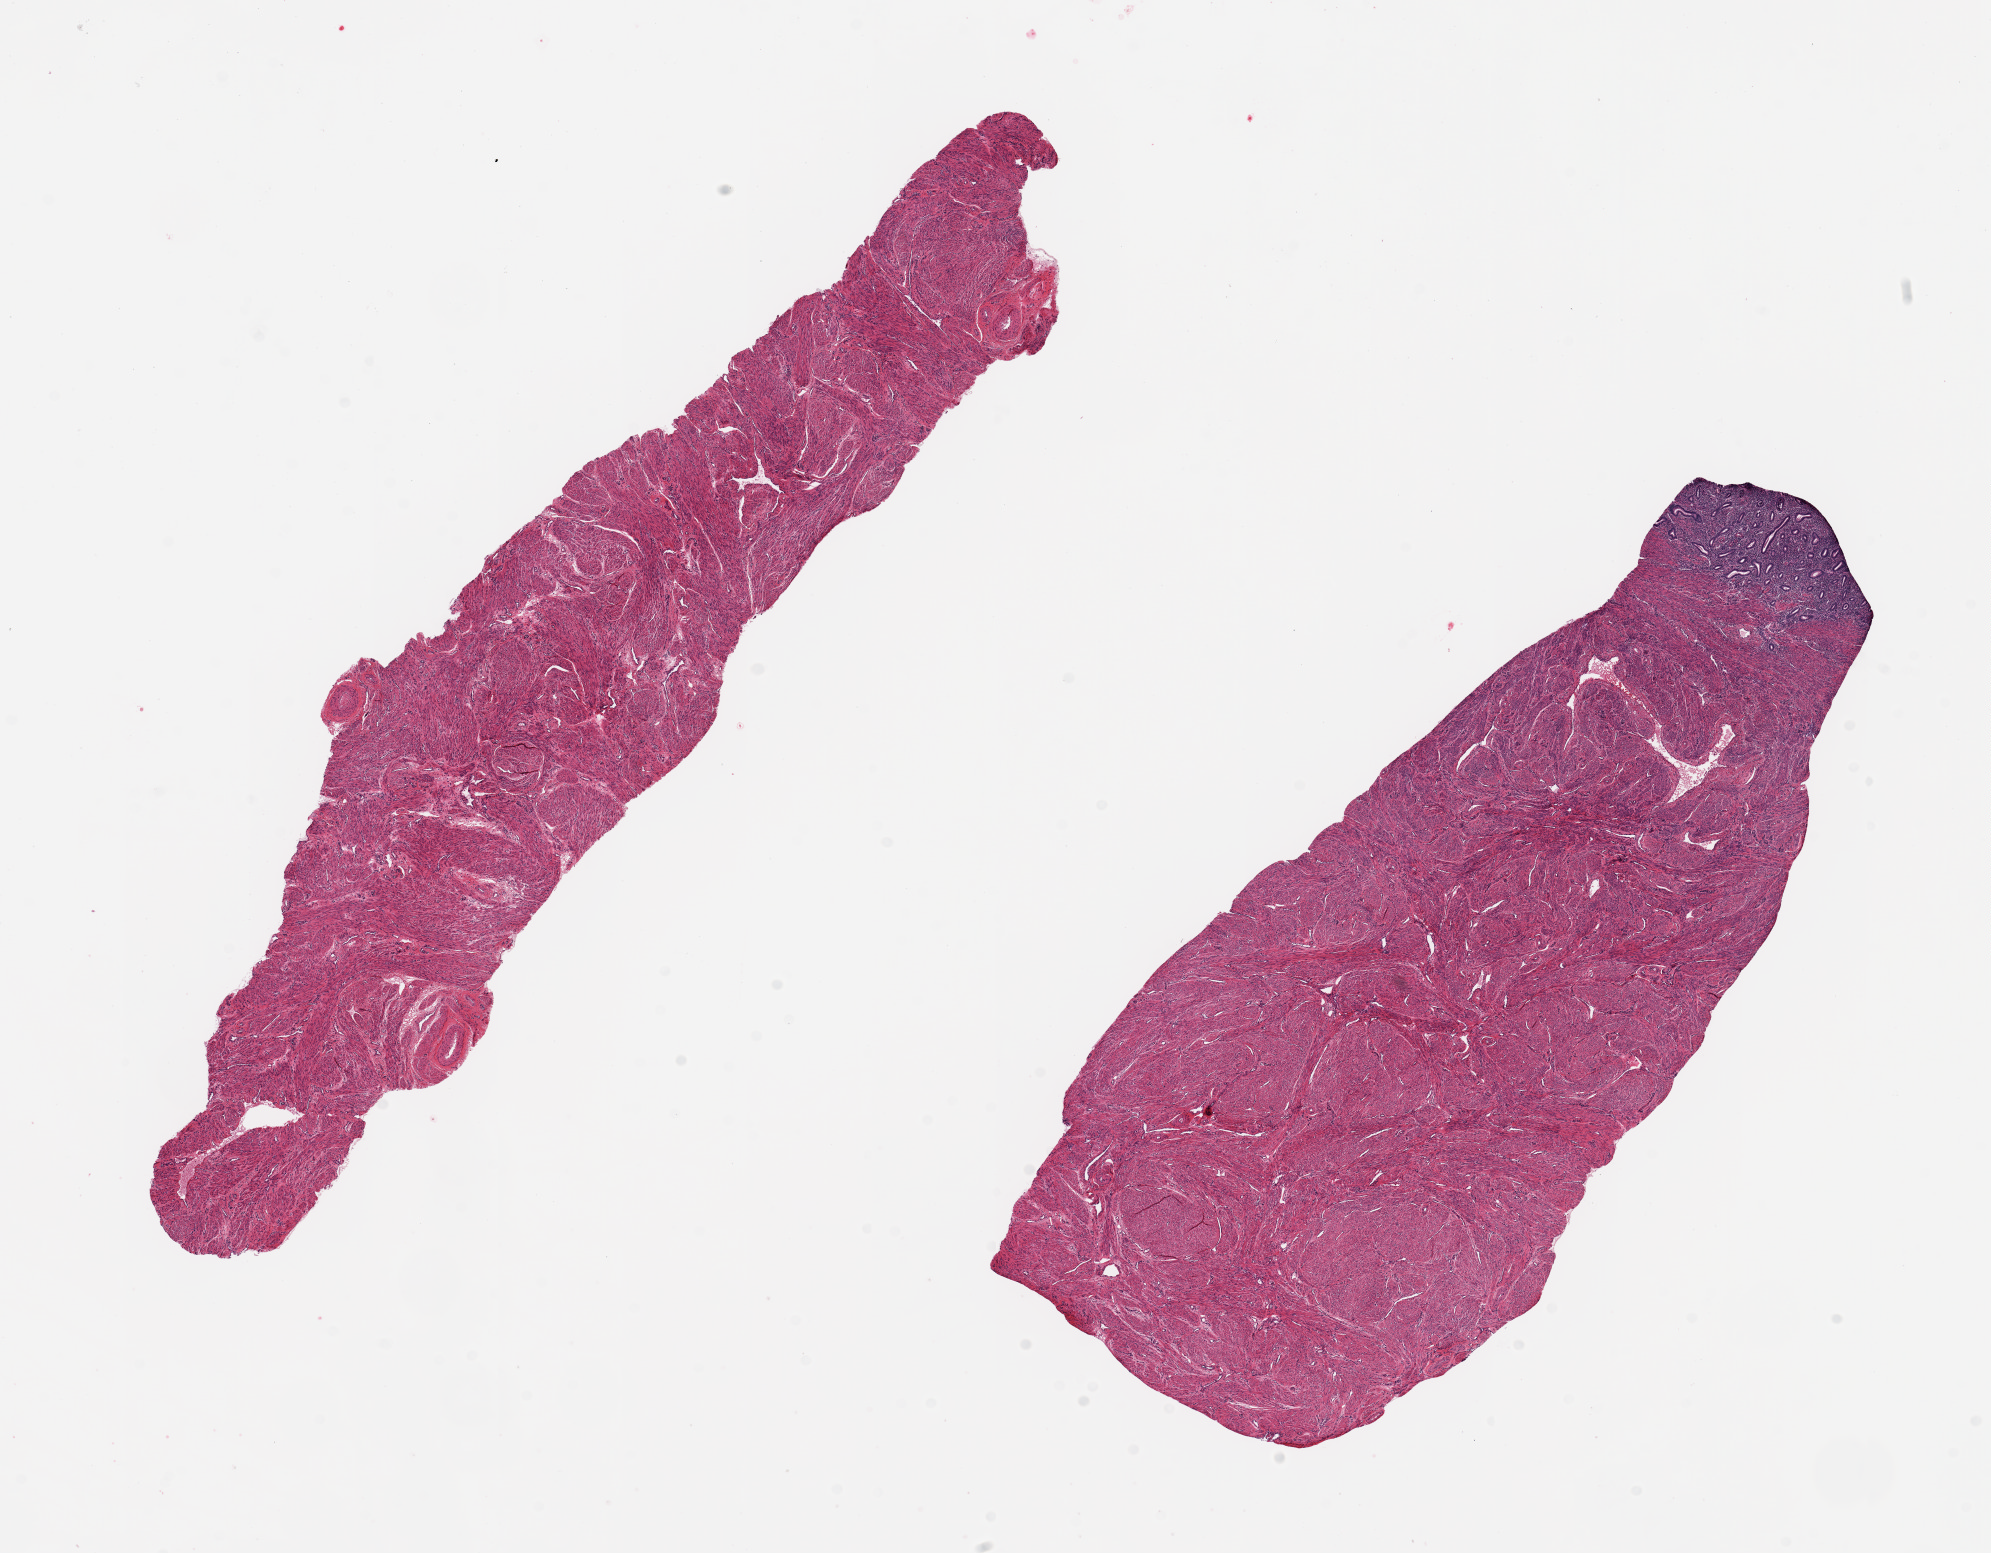
Whole-slide image, H&E stain — whole scanned area (about 15.8 x 12.3 mm) shown as a low-resolution overview, PAXgene-fixed paraffin-embedded (PFPE) section, sampled site (target tissue): uterus, donor tissue sample. Donor sex: female.
Pathologist's review note for this sample: 2 pieces; only one, 8.7x3.8 mm, has endometrium, 0.8x1.8mm; other all muscle.